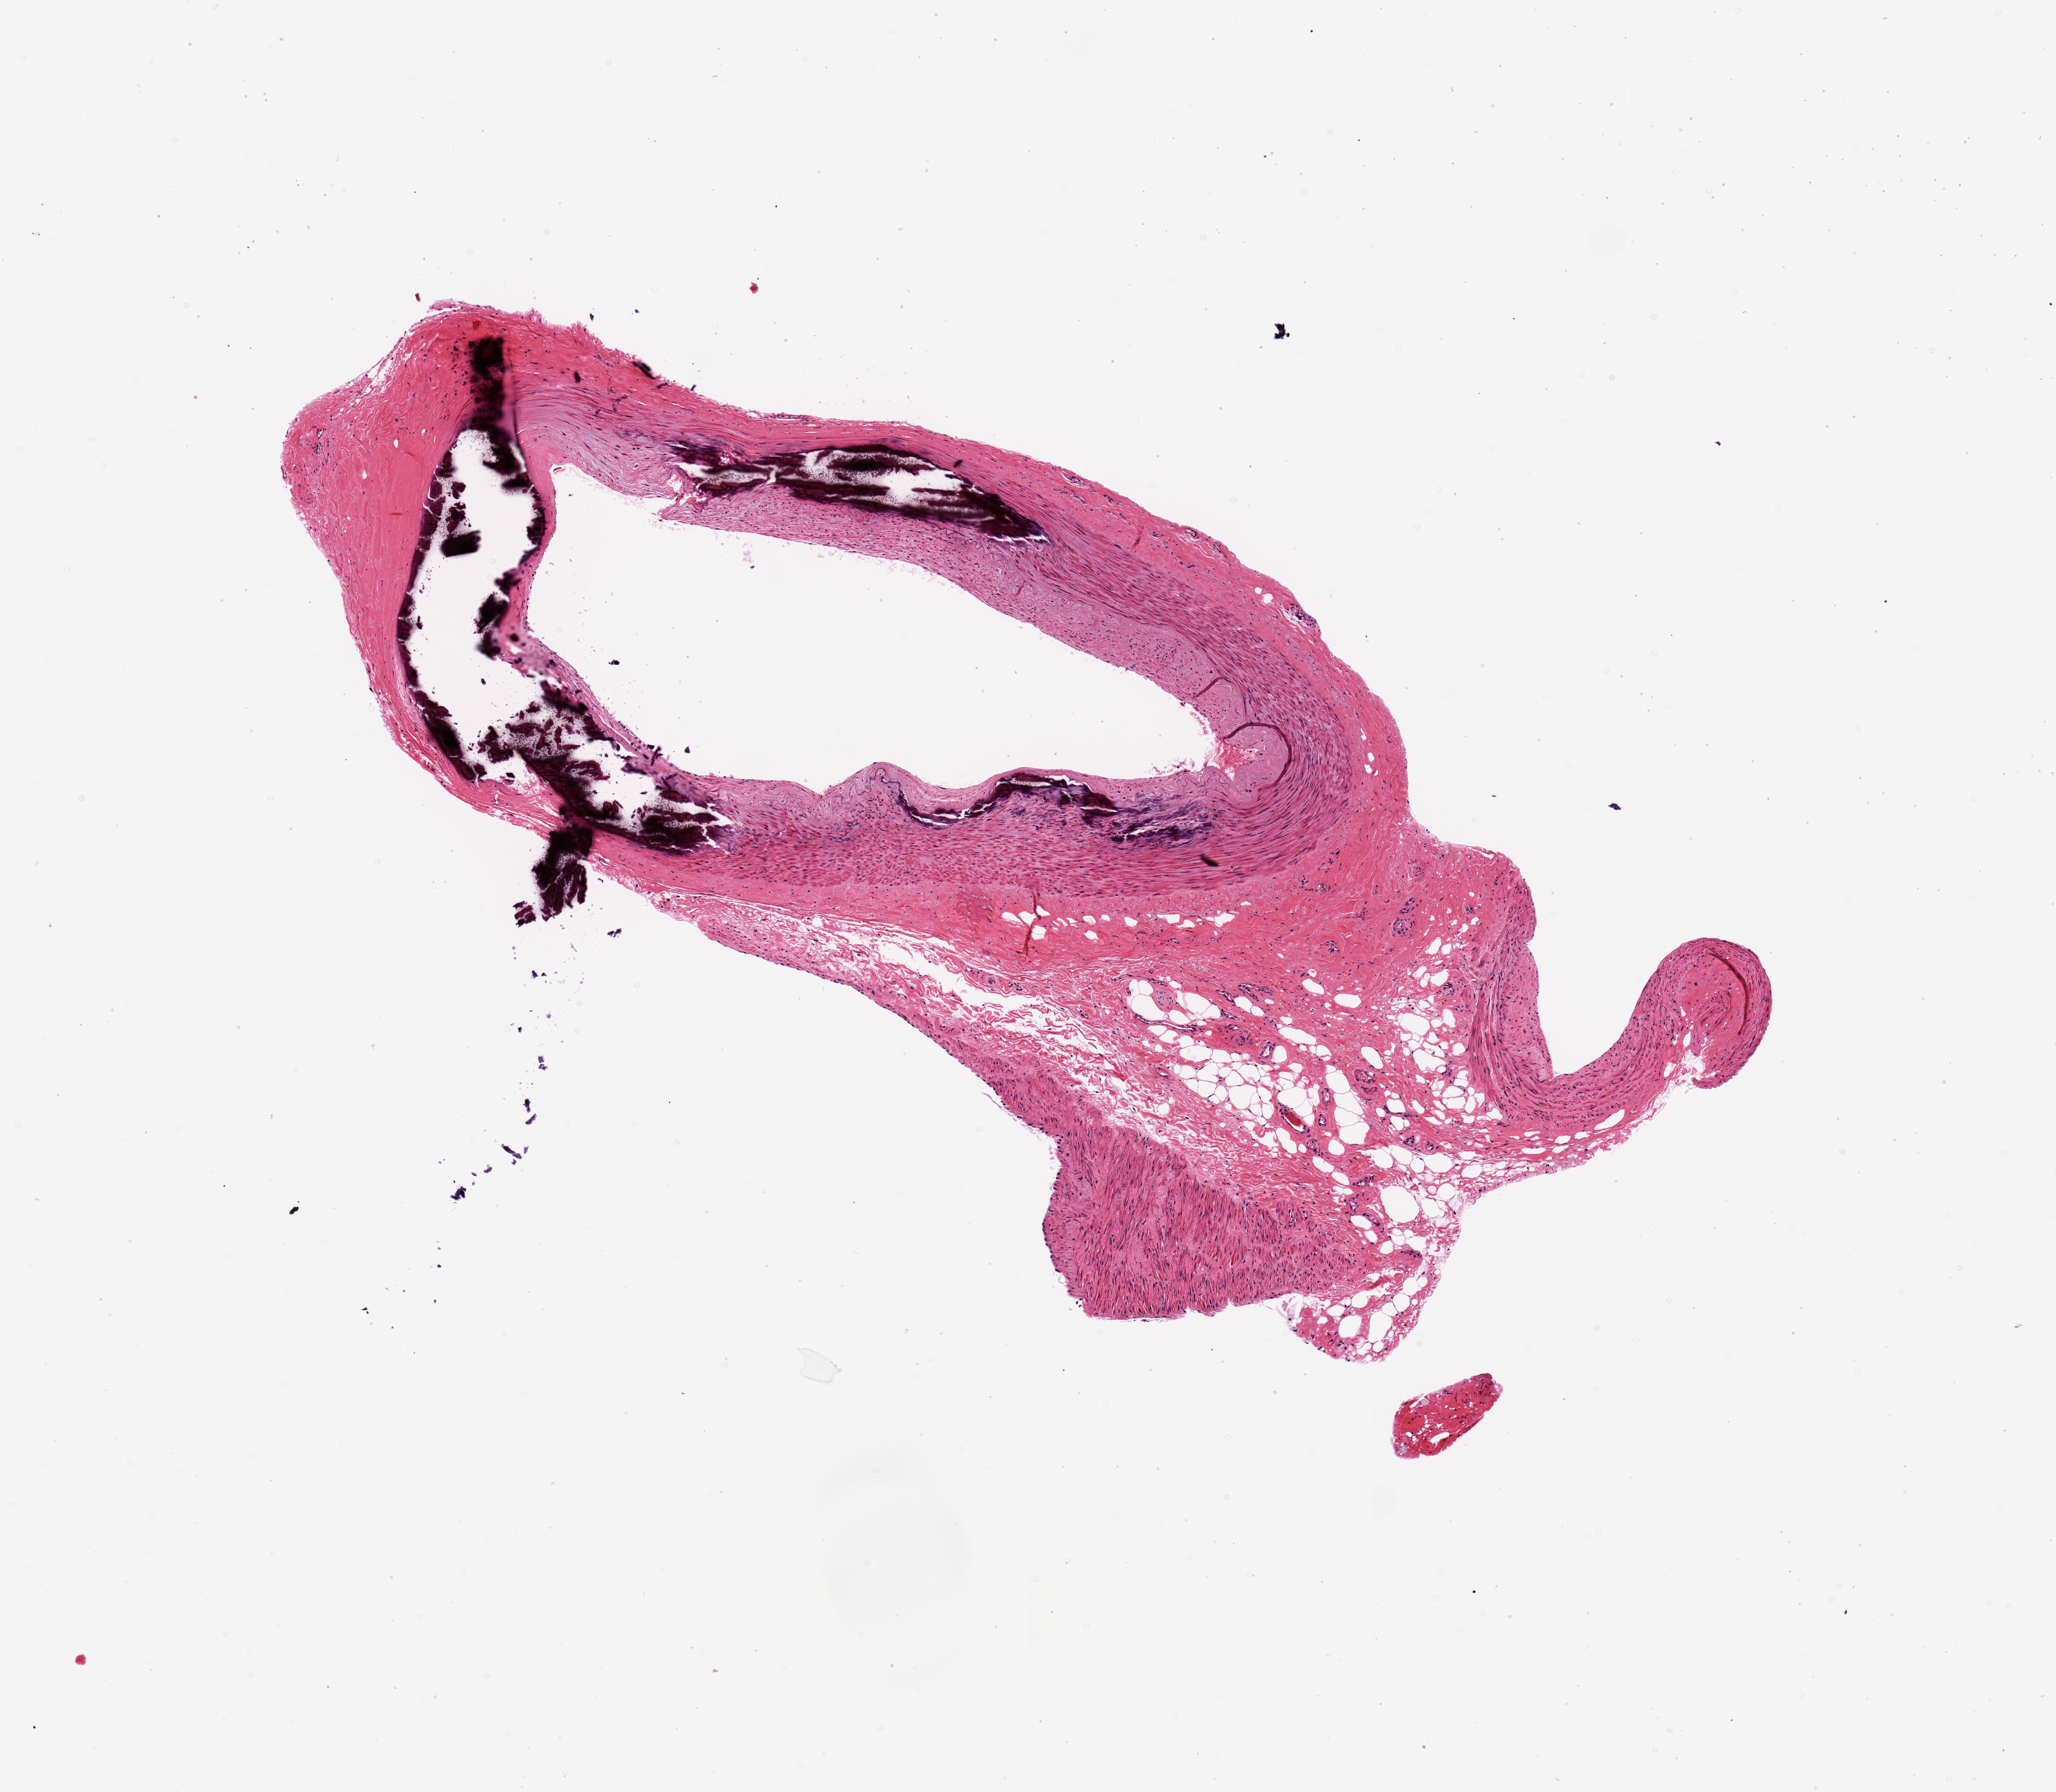
Digitized H&E-stained section, low-resolution overview of the scanned area, about 5.9 x 5.1 mm (slide scanned at 20x). PAXgene-fixed paraffin-embedded (PFPE) section. Sampled site (target tissue): tibial artery. Tissue donor sample. Donor: male.
Review note (as recorded): large calcifications.